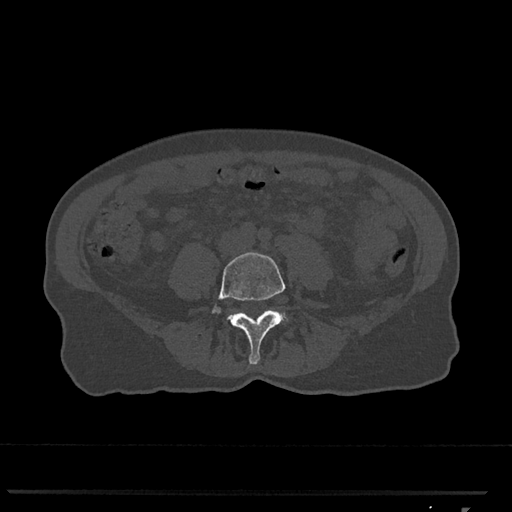
CT including the spine, one axial slice. Position 202 of 793 along the scan axis. 120 kVp. Bone window (W 1800 / L 400 HU). 512 × 512 image matrix, field of view 380 × 380 mm. Female patient, age 62 years. Case-level facts recorded for this patient, not image findings: primary cancer: renal.
Outlined on this slice (semi-automatically segmented with operator editing):
- L4 vertebra: bounding box [x1, y1, x2, y2] px = [211, 252, 286, 365]
- L5 vertebra: [282, 313, 285, 319]